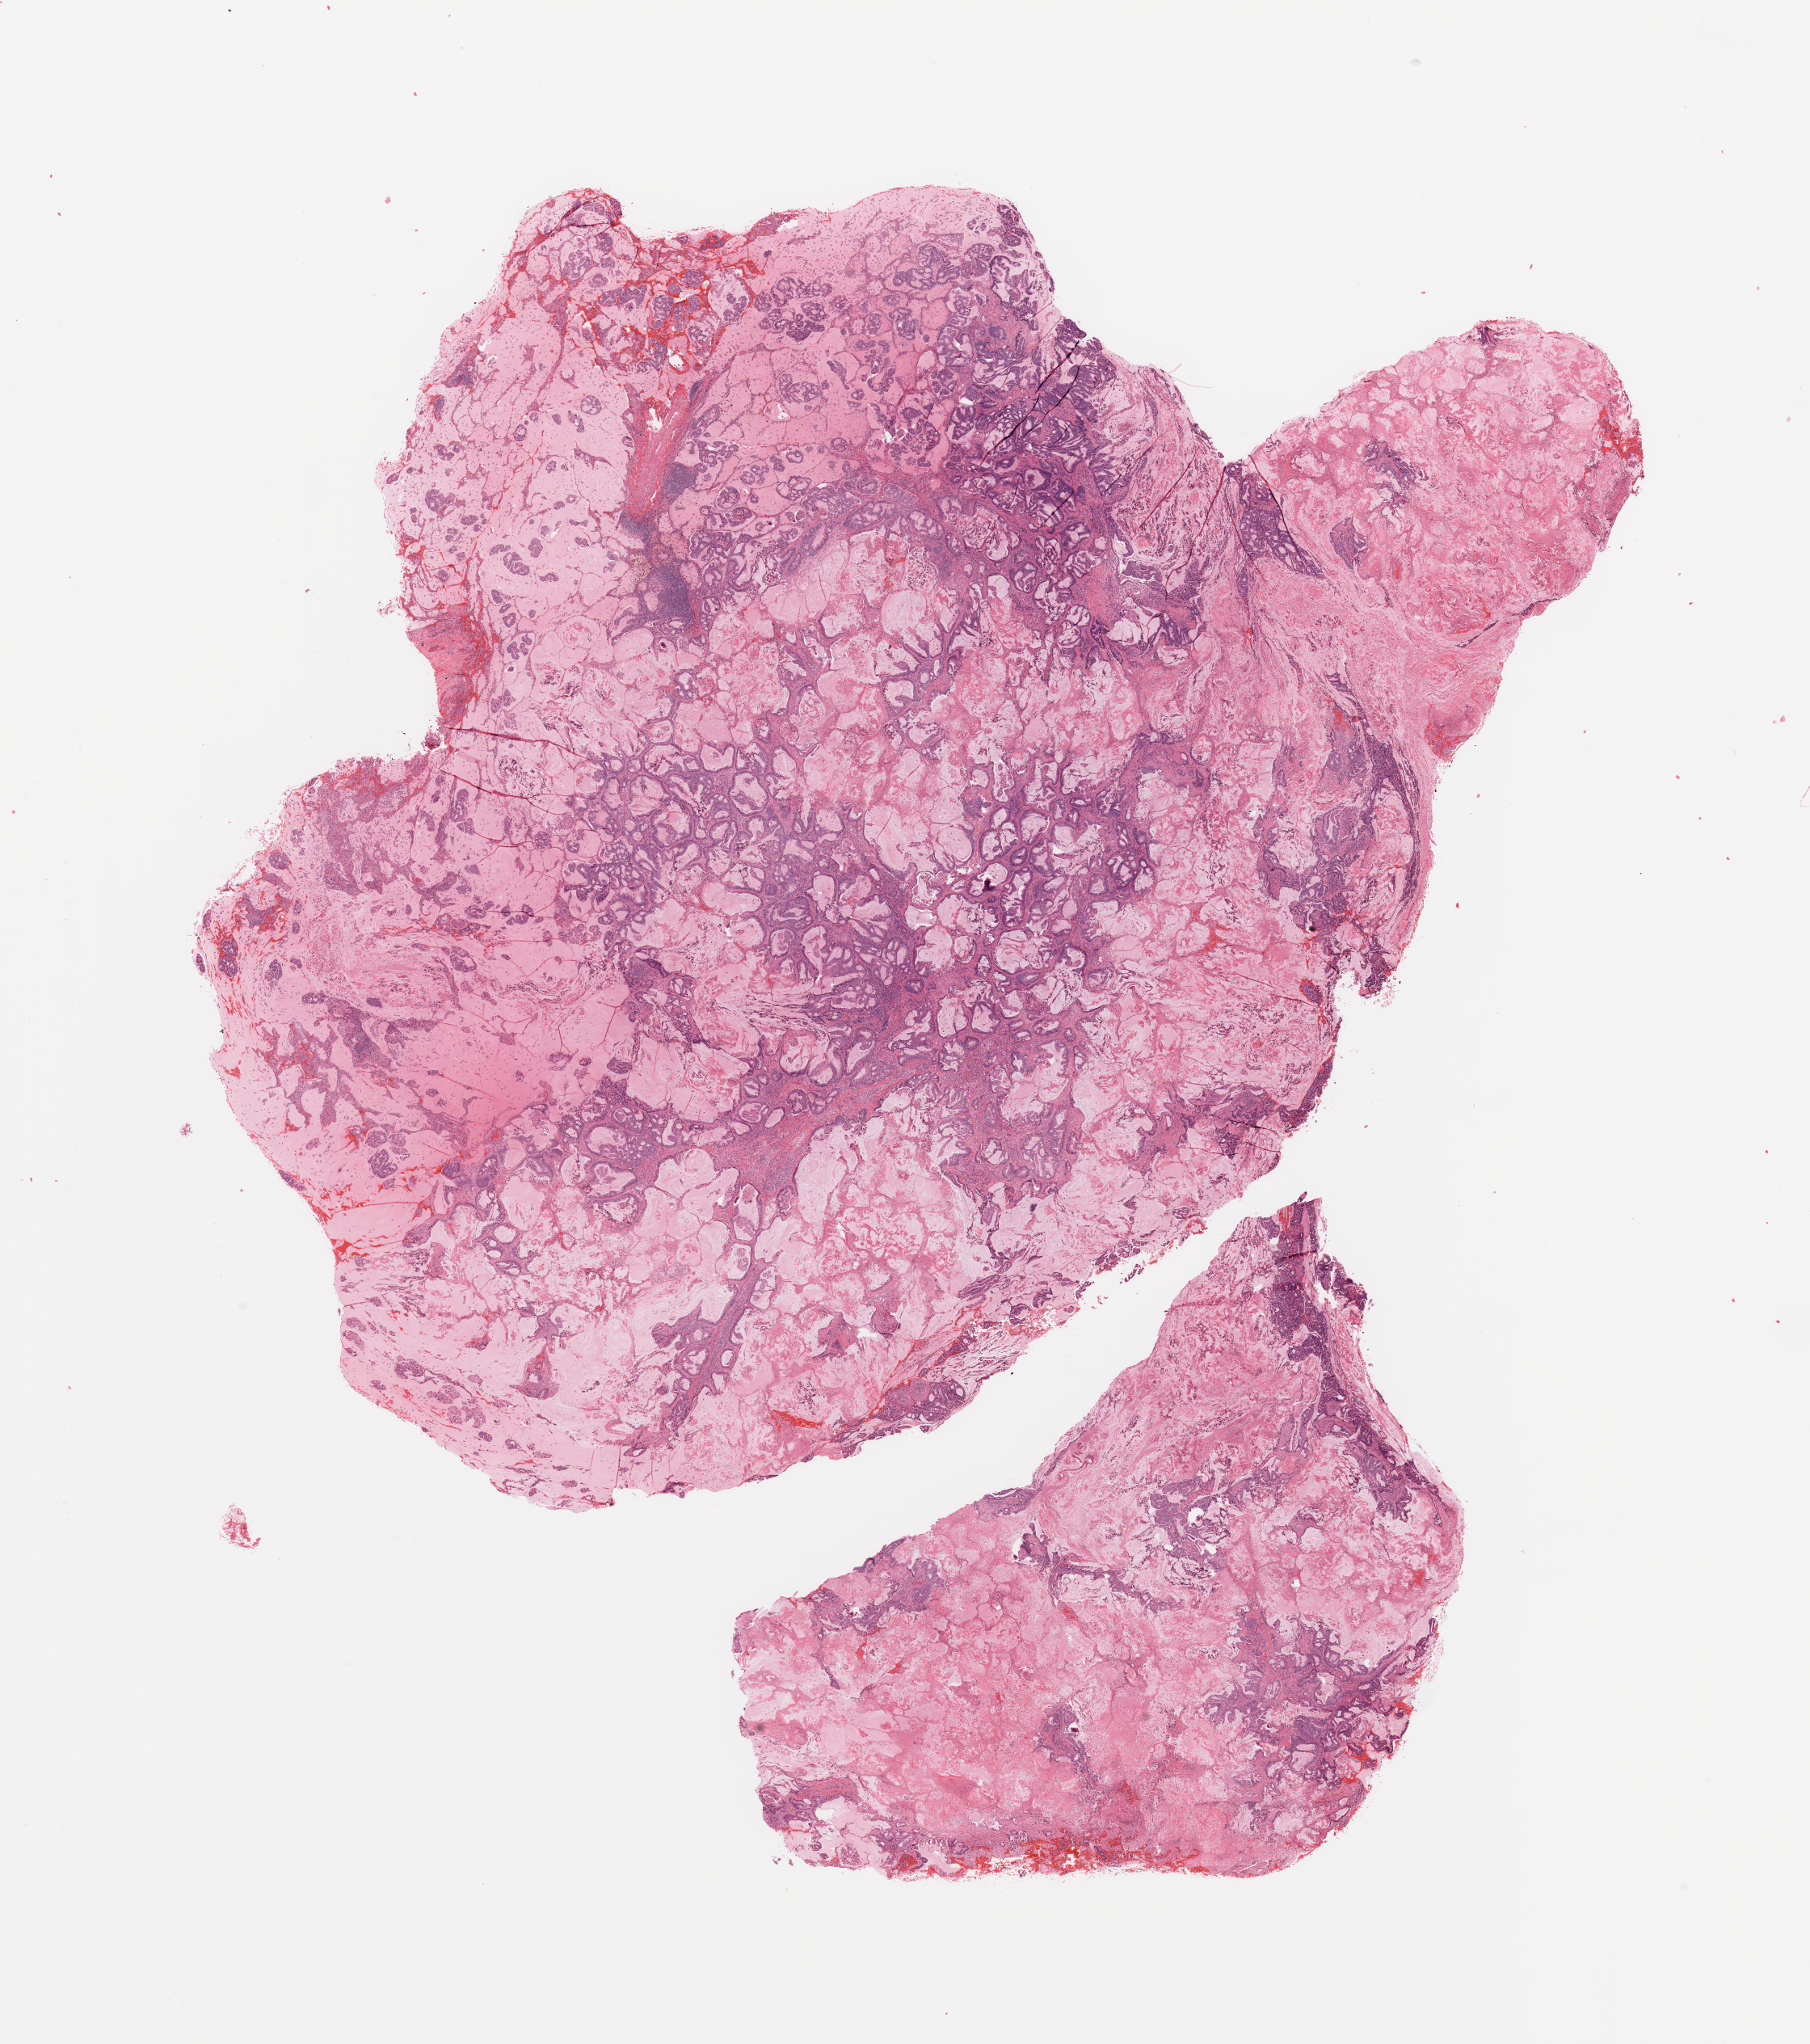
Digitized H&E tissue section (whole slide) — shown as a low-resolution overview of the whole scanned area (about 17.7 x 20.0 mm, slide scanned at 20x); tumour tissue sample, lung. Male, 40 y/o. Histologic grade: G2 (moderately differentiated).
* histologic diagnosis: Adenocarcinoma, NOS
* AJCC pathologic stage: IB
* primary tumour site (as recorded): right lower lobe